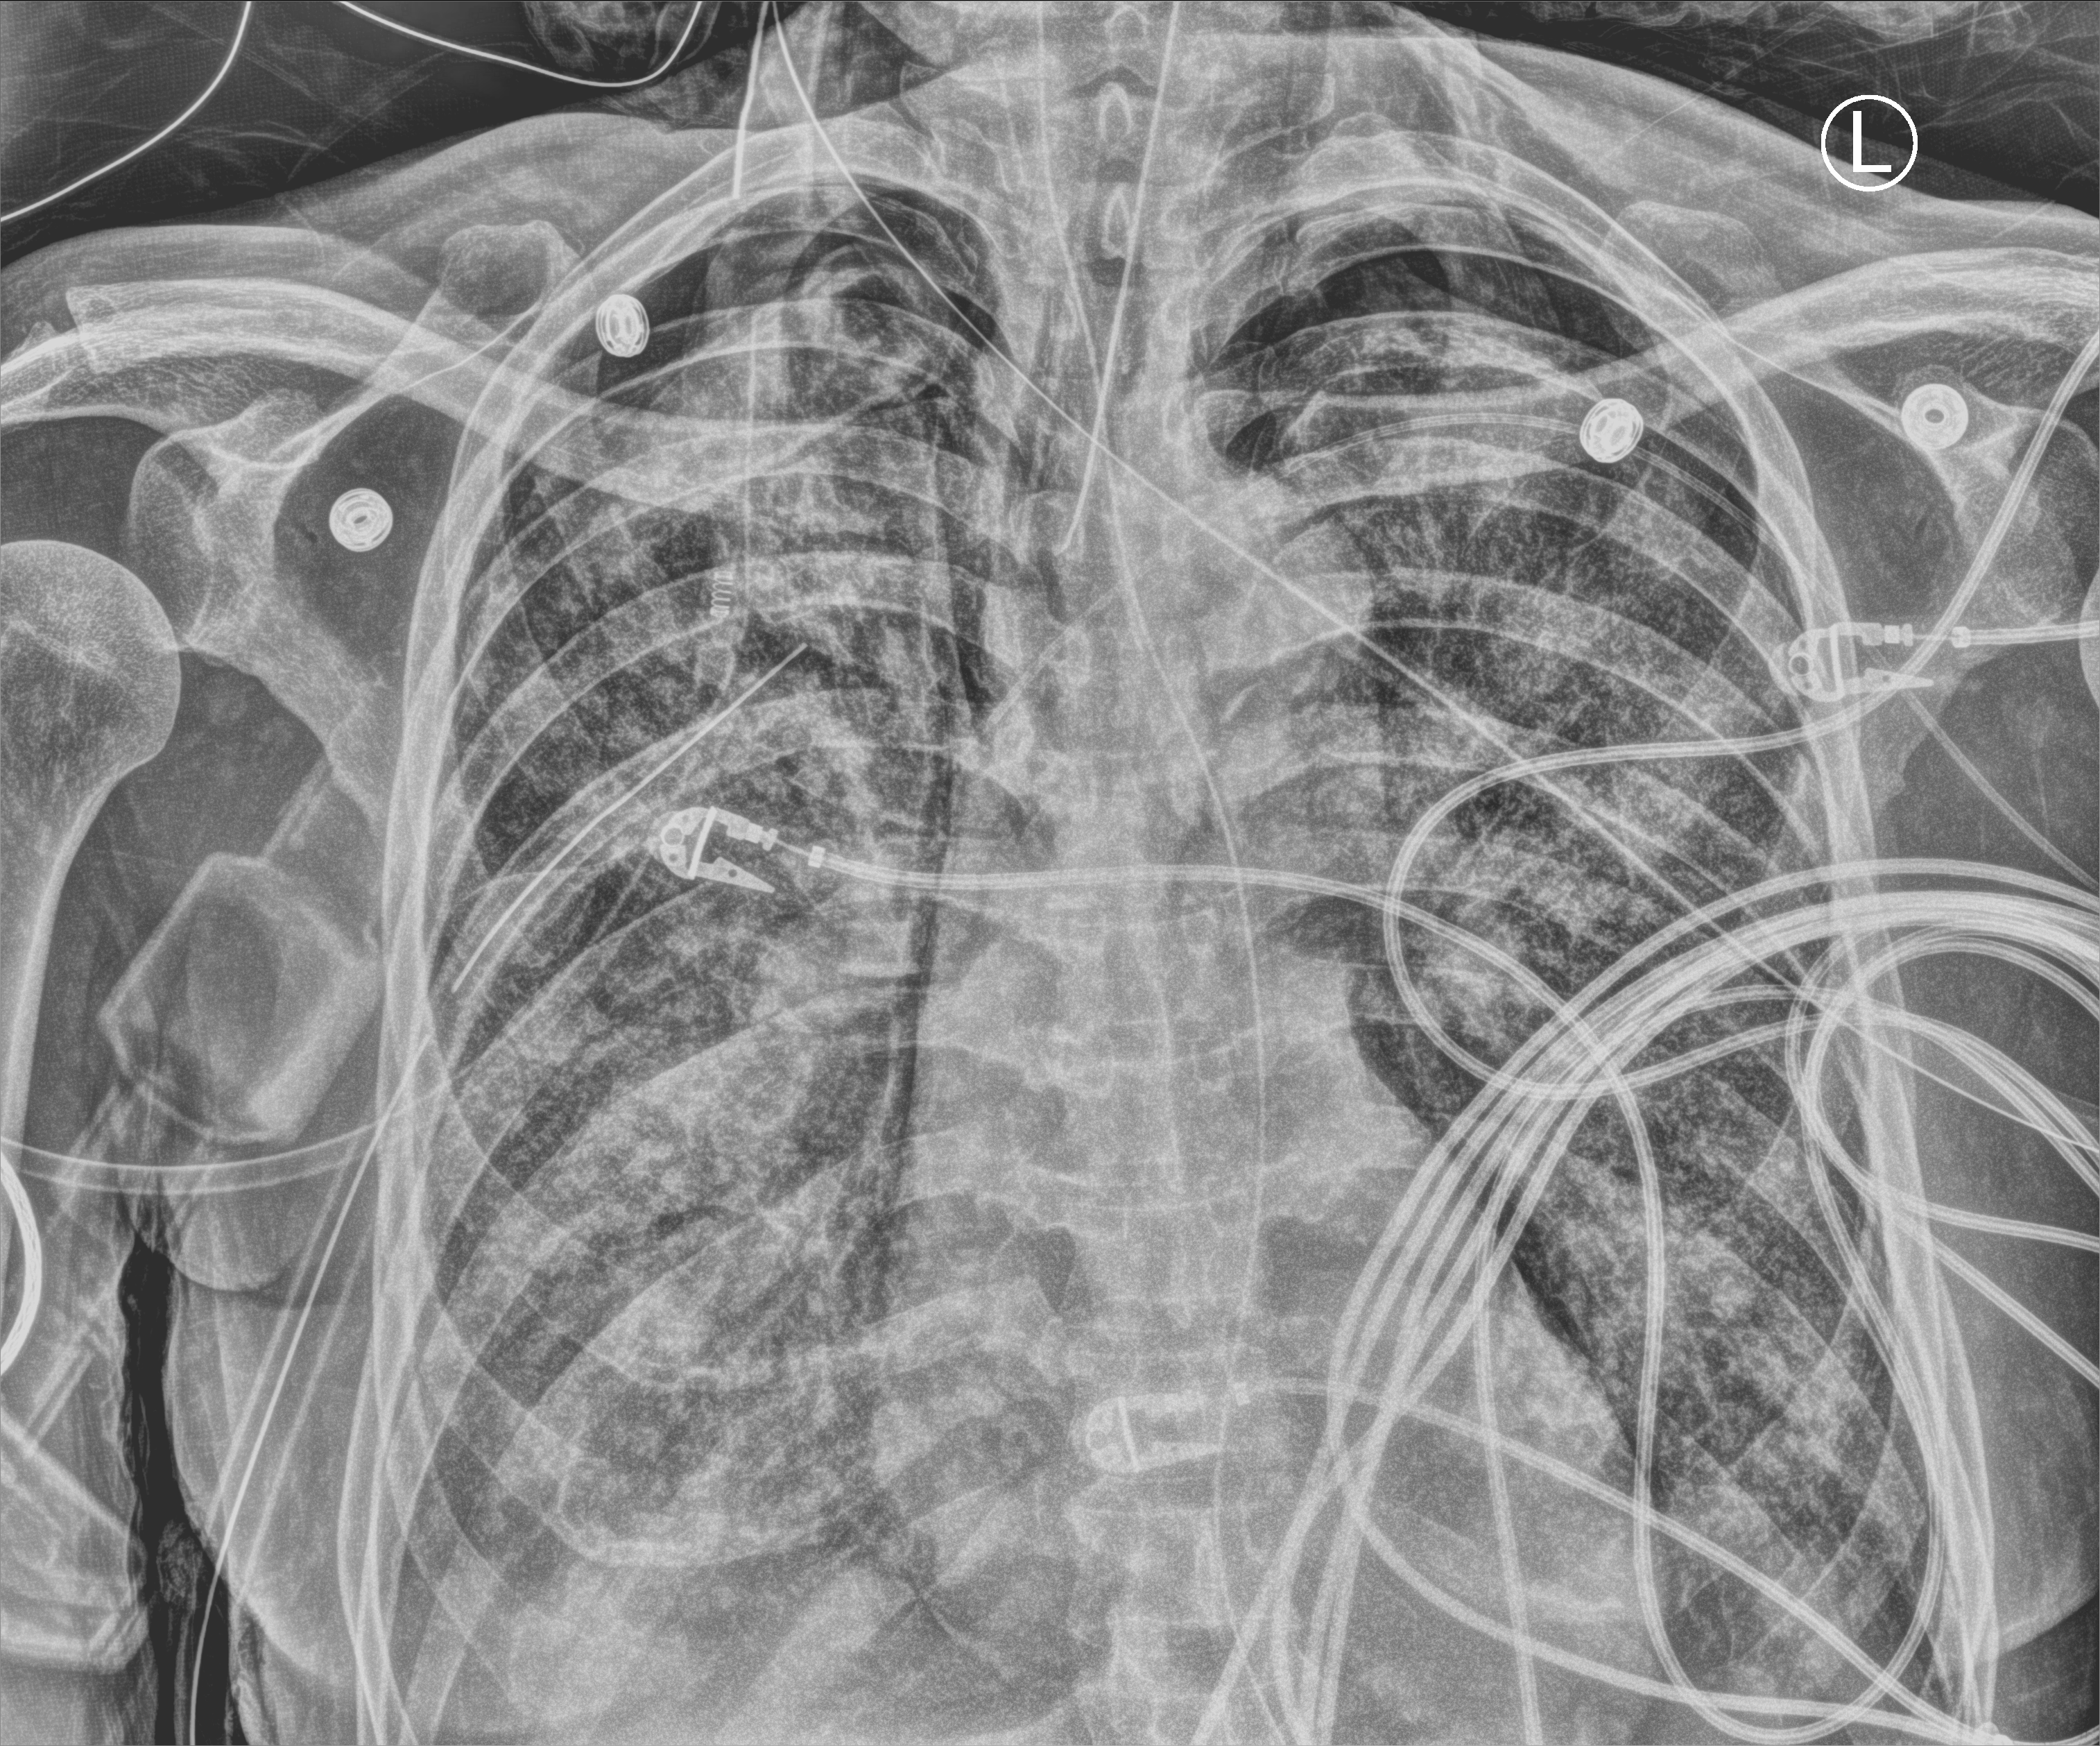
Bedside chest radiograph (computed radiography); anteroposterior (AP) projection. Male patient hospitalised with COVID-19, age 60–74 years.
Admission-level facts for this patient (not findings on this image; timing relative to this image not recorded): mechanically ventilated during this hospital stay: yes.